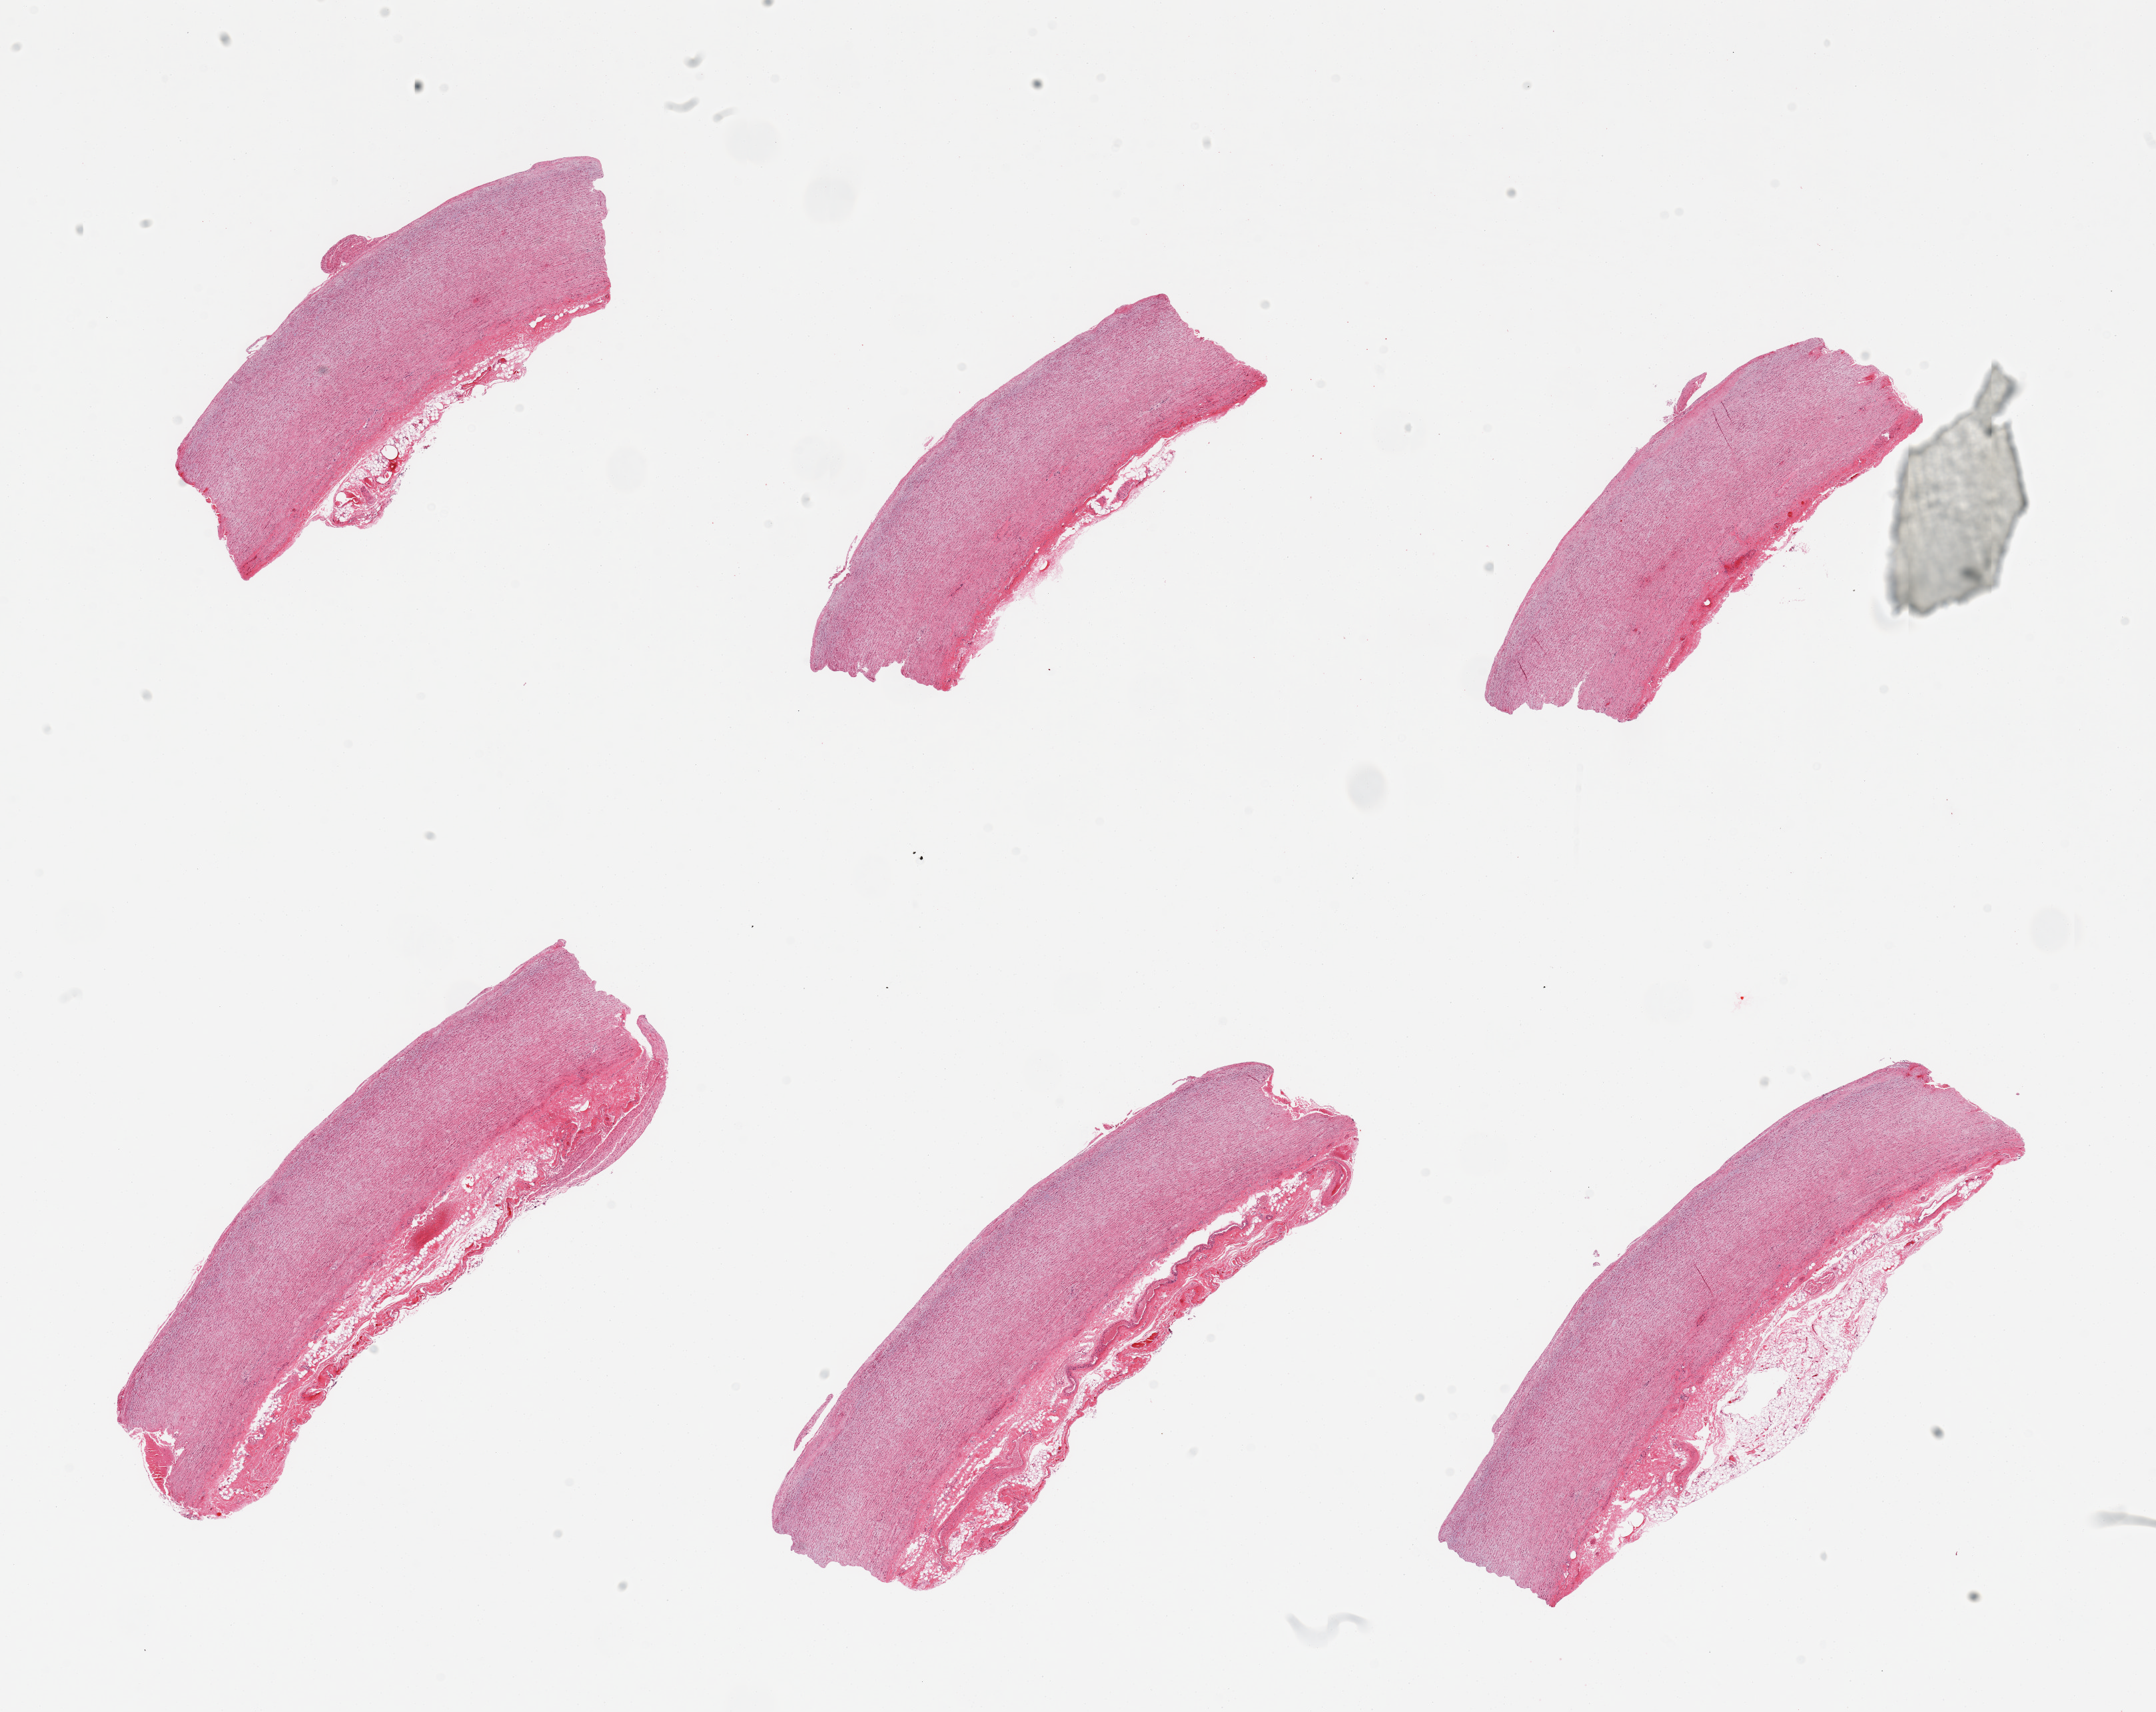
Haematoxylin and eosin whole-slide image, low-resolution overview of the scanned area, about 25.6 x 20.3 mm; PAXgene-fixed paraffin-embedded (PFPE) section; sampled site (target tissue): aorta; donor tissue sample. Male donor.
Review note (as recorded): 6 pieces, some attached adventitia.